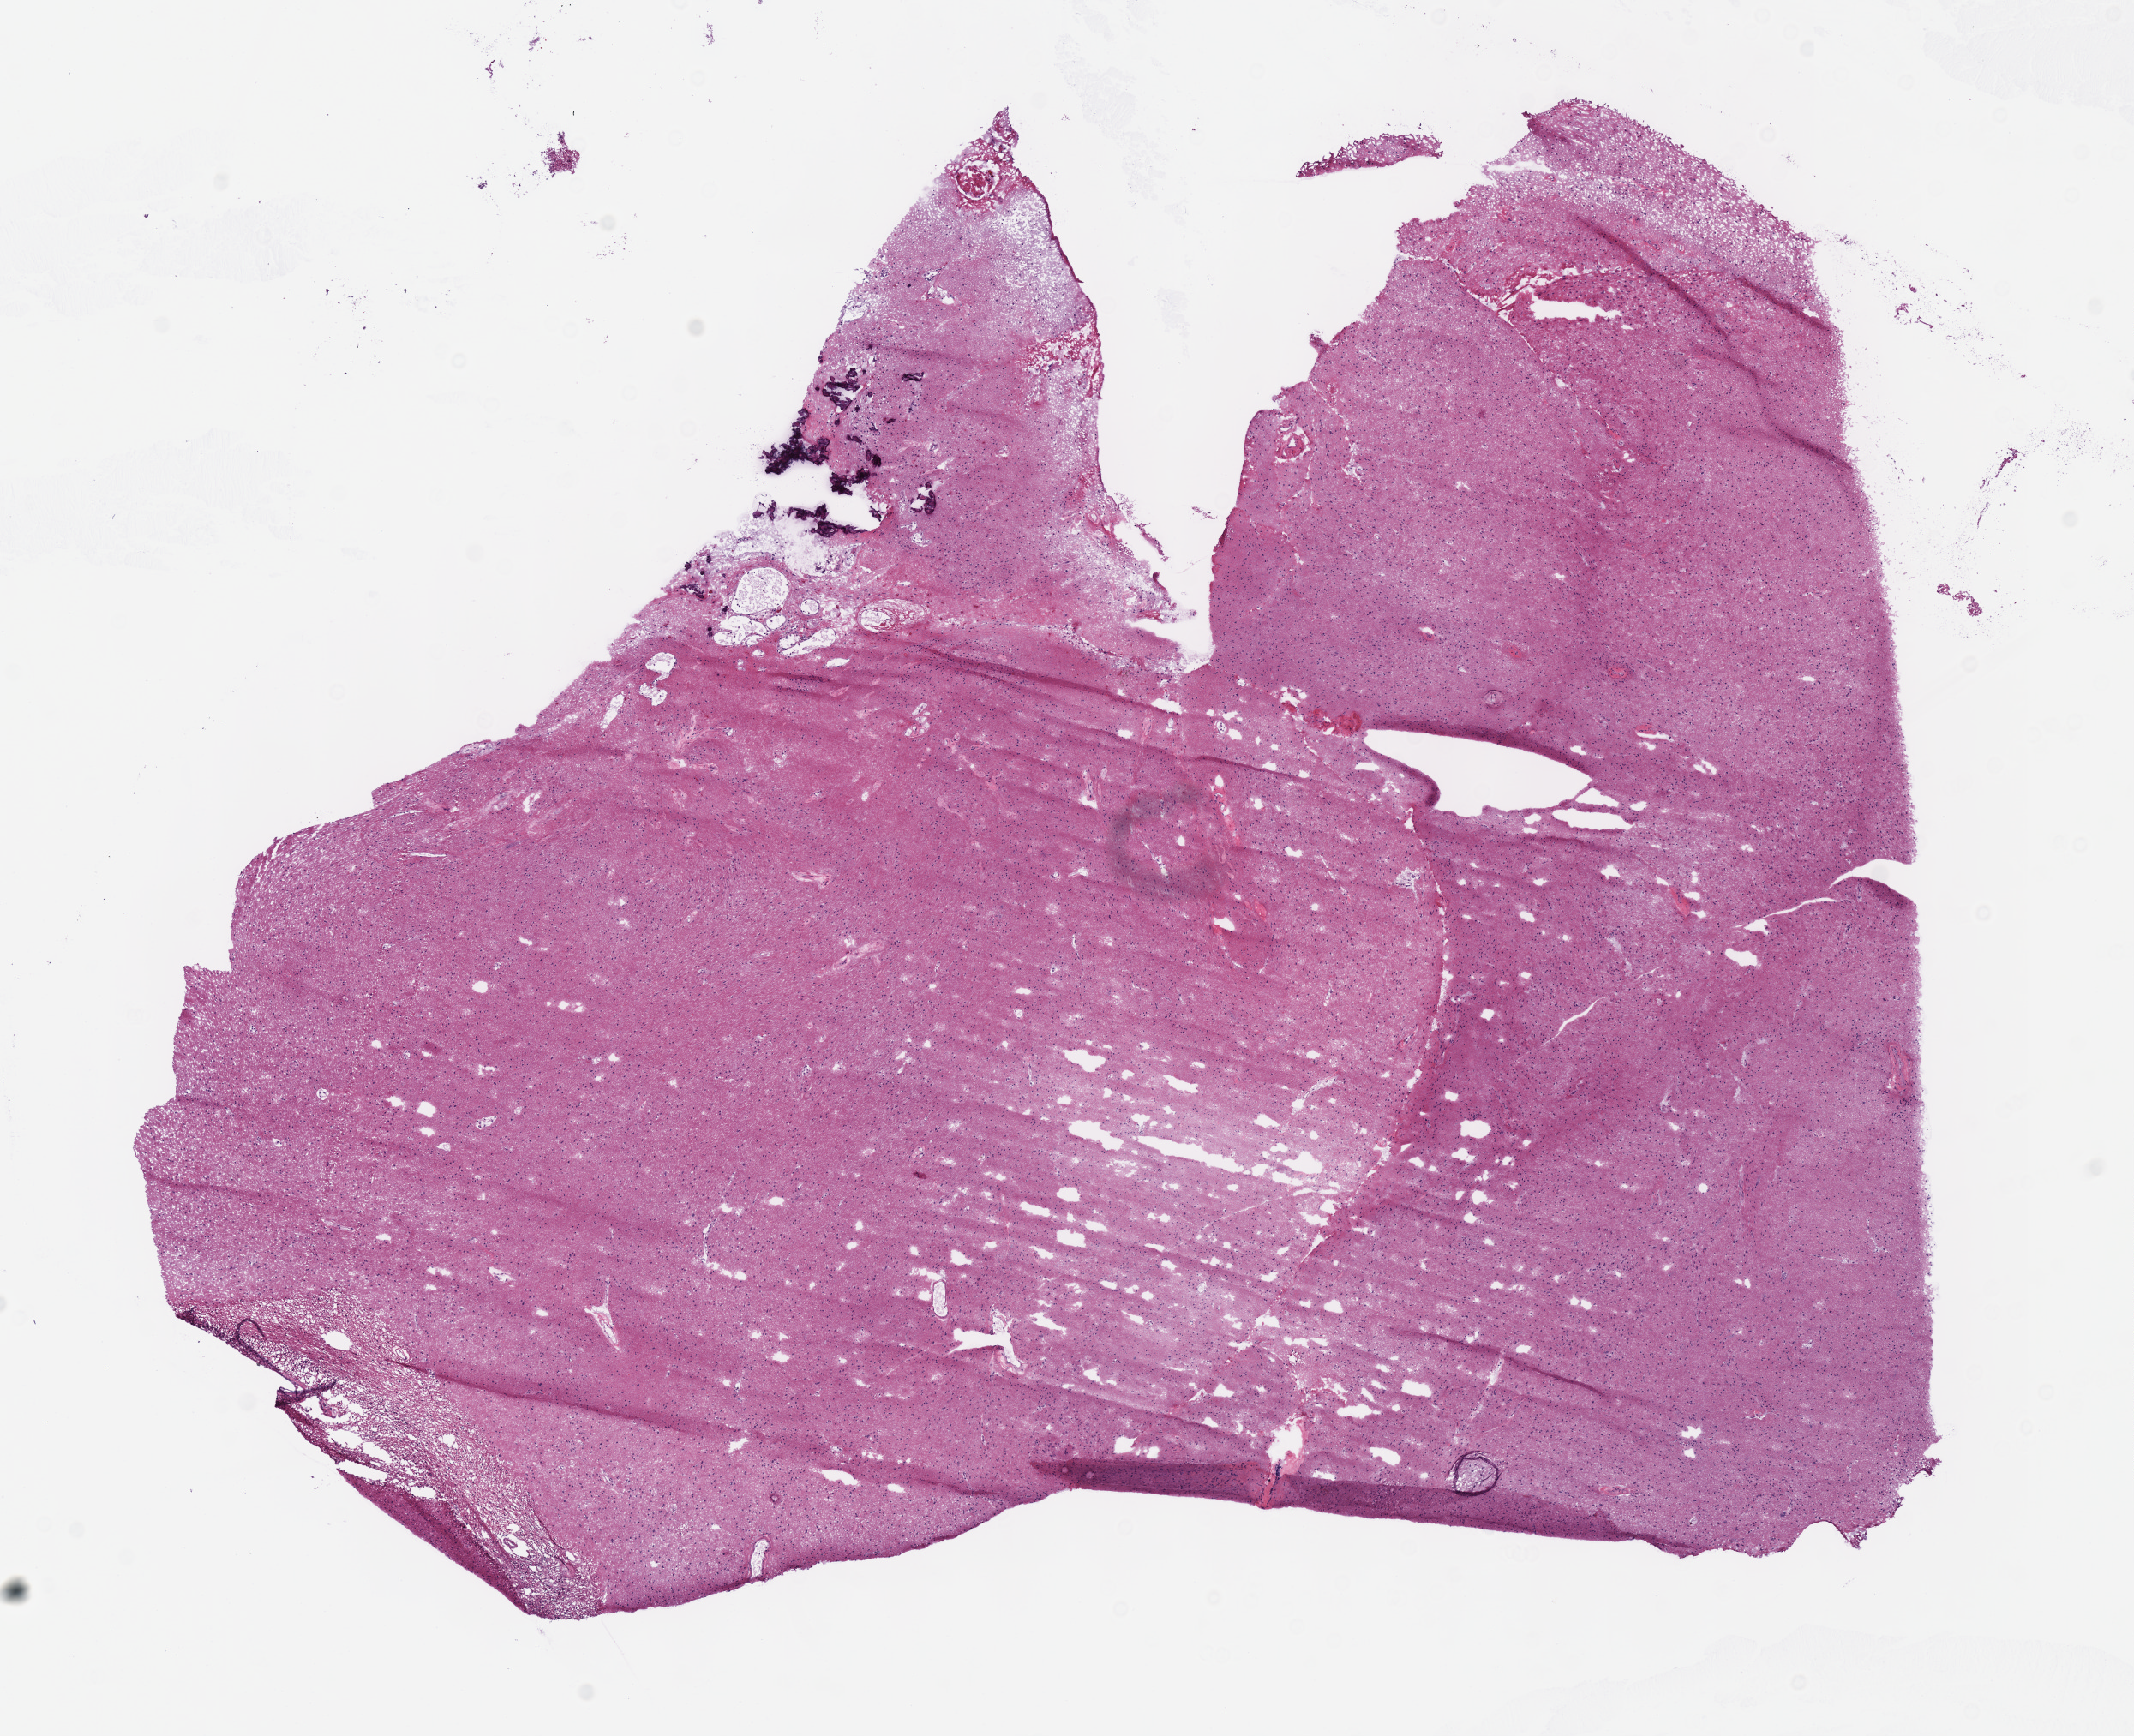
Digitized H&E-stained tissue section (whole slide) — a low-resolution overview of the entire scanned area, about 9.8 x 8.0 mm, frozen section from the top of the tissue portion, primary tumour sample from the brain. Female patient; age at initial diagnosis 32 years. Histologic grade: G2 (moderately differentiated). Composition of this section per pathologist review: tumour cells 100%, tumour nuclei 60%, normal cells 0%, stromal cells 0%, necrosis 0%.
Pathologic diagnosis: Astrocytoma, NOS.